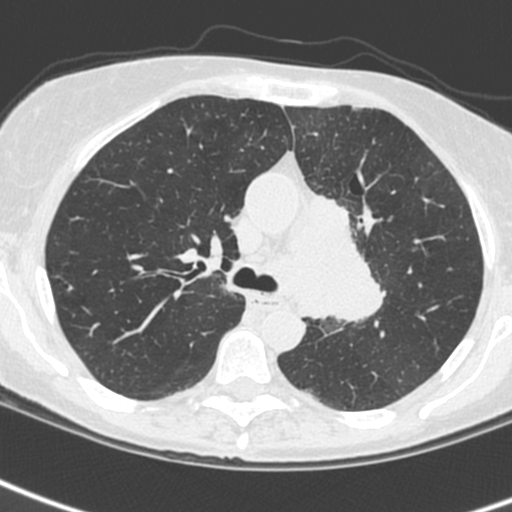
Low-dose screening chest CT, one axial slice. Position 163 of 242 along the scan axis. Lung window (W 1500 / L -600 HU). 1.3 mm slice thickness. 512 × 512 image matrix.
Outlined on this slice (manually delineated by an expert):
- lesion 3 (tumor, upper lobe of left lung): bounding box [x1, y1, x2, y2] px = [305, 193, 384, 323]